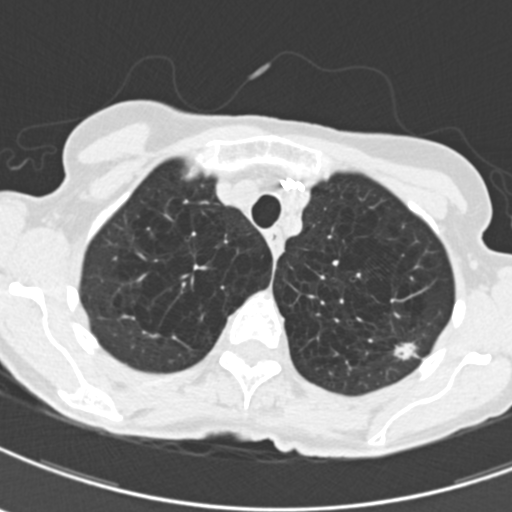
Low-dose screening chest CT, axial slice; third annual screen; lung window (W 1500 / L -600 HU); standard (soft-tissue) reconstruction kernel (B30f); slice 40 of 203 in the series; 512 × 512 image matrix, field of view 279 × 279 mm. Female, age 71 years at enrolment. Current smoker at enrolment.
- Expert reader's lesion annotation, box from (x=387, y=329) to (x=431, y=370) px.
- The exam's reader record, not a measurement of the box and not confirmed to be the same lesion: non-calcified nodule or mass ≥4 mm, left upper lobe, 12 × 9 mm, spiculated (stellate) margins, mixed attenuation, pre-existing on the prior screen: yes; interval growth: yes.
- Official screen result: positive, other.
- Participant outcome: lung cancer diagnosed 114 days after this screen — adenocarcinoma, NOS, left upper lobe, moderately differentiated (G2), stage IA (AJCC 6th edition), 12 mm at pathology.